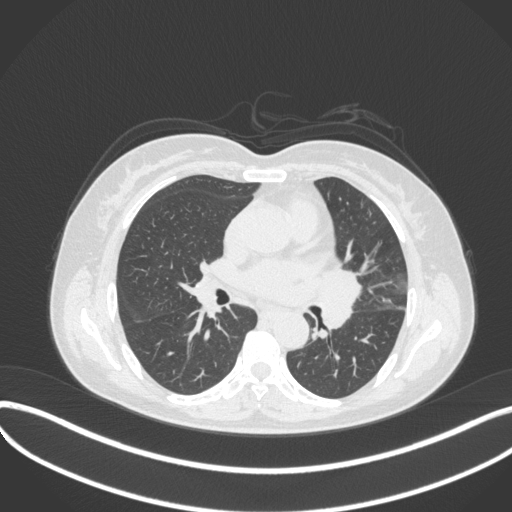
Chest CT, one axial slice. Position 187 of 373 along the scan axis. Lung window (W 1500 / L -600 HU). 1 mm slice thickness. 512 × 512 image matrix, field of view 400 × 400 mm. Patient: female, 54 years. From the clinical record (not read from this slice): clinical TNM (as recorded): T2a N1 M0; histopathological grade: G3.
Structures marked on this image (rectangle marked by the reading radiologist):
- lung tumour (recorded histology: small cell carcinoma): bounding box [x1, y1, x2, y2] px = [316, 263, 362, 333]